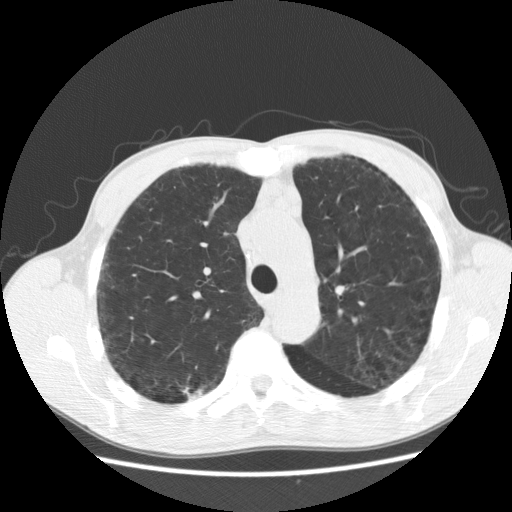
Chest CT (low-dose screening protocol), one axial image, second screening round (one year after baseline), lung window (W 1500 / L -600 HU). Male, age 60 years at enrolment. Current smoker at enrolment.
- Lesion marked by an expert reader, box from (x=170, y=375) to (x=212, y=407) px.
- Screening reader's record for this exam (one nodule recorded; not confirmed to be the boxed lesion): non-calcified nodule or mass ≥4 mm, right upper lobe, 8 × 5 mm, poorly defined margins, soft tissue attenuation, pre-existing on the prior screen: yes; interval growth: yes.
- Official screen result: positive, other.
- Later outcome: lung cancer diagnosed 204 days after this screen — squamous cell carcinoma, NOS, right upper lobe, well differentiated (G1), stage IA (AJCC 6th edition), 15 mm at pathology.